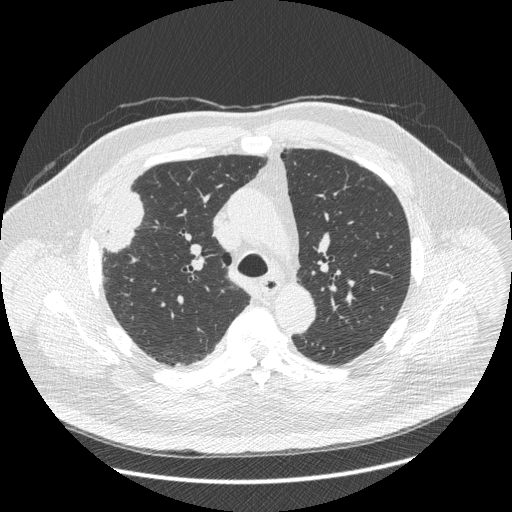
Axial slice from a low-dose chest CT screening exam, third screening round (two years after baseline), lung window (W 1500 / L -600 HU), 1.25 mm slice thickness, standard (soft-tissue) reconstruction kernel (STANDARD), 120 kVp, 512 × 512 image matrix, field of view 400 × 400 mm. Male, age 66 years at enrolment. Current smoker at enrolment.
Lesion marked by an expert reader, bounding box [x1, y1, x2, y2] px = [87, 195, 146, 267]. Screening reader's record for this exam (one nodule recorded; not confirmed to be the boxed lesion): non-calcified nodule or mass ≥4 mm, right upper lobe, 48 × 25 mm, spiculated (stellate) margins, soft tissue attenuation, pre-existing on the prior screen: no. Official screen result: positive, other. Lung cancer was diagnosed 35 days after this screen: non-small cell carcinoma, right upper lobe, stage IV (AJCC 6th edition), 50 mm at pathology.